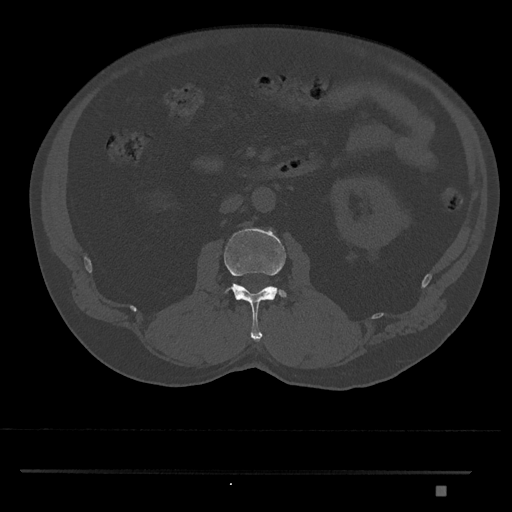
CT including the spine, one axial slice; position 745 of 1134 along the scan axis; 120 kVp; bone window (W 1800 / L 400 HU); 0.5 mm slice thickness; 512 × 512 image matrix, field of view 429 × 429 mm. Male patient, age 65 years. Case-level facts recorded for this patient, not image findings: primary cancer: prostate.
Structures marked on this image (semi-automatically segmented with operator editing):
- L2 vertebra: box from (x=224, y=228) to (x=287, y=342) px